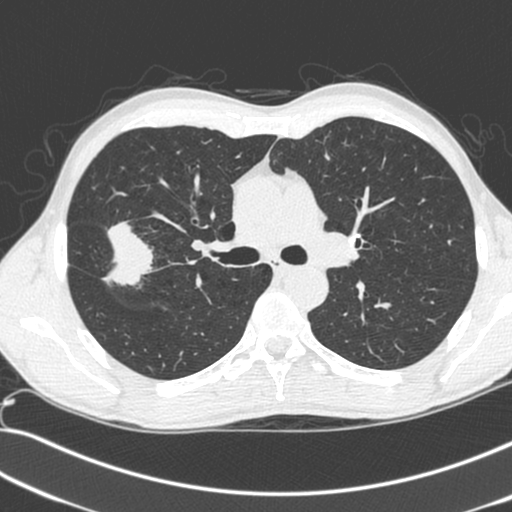
Axial slice from a low-dose chest CT screening exam. First (baseline) screen. Lung window (W 1500 / L -600 HU). 1.3 mm slice thickness. 120 kVp. Slice 92 of 281 in the series. Male, age 55 years at enrolment.
- Expert reader's lesion annotation, bounding box (x1, y1, x2, y2) in pixels: (67, 219, 157, 297).
- The exam's reader record, not a measurement of the box and not confirmed to be the same lesion: non-calcified nodule or mass ≥4 mm, right upper lobe, 52 × 39 mm, spiculated (stellate) margins, soft tissue attenuation.
- Official screen result: positive, change unspecified: nodule(s) >= 4 mm or enlarging nodule(s), mass(es), or other non-specific abnormalities suspicious for lung cancer.
- Lung cancer was diagnosed 25 days after this screen: large cell neuroendocrine carcinoma, right upper lobe, poorly differentiated (G3), stage IIB (AJCC 6th edition), 49 mm at pathology.